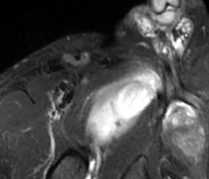
MRI of an extremity soft-tissue mass, one axial slice; position 71 of 89 along the scan axis; STIR; MR volume resampled by the dataset authors to the PET/CT grid (not the native acquisition matrix); 3.27 mm slice thickness; 209 × 179 image matrix, field of view 204 × 175 mm. Male patient. Case-level facts recorded for this patient, not image findings: histological type: undifferentiated - pleiomorphic; grade: high; site of the primary tumour: right thigh.
Outlined on this slice (expert contour drawn on MRI and transferred to this co-registered scan by the dataset authors):
- gross tumour volume including surrounding oedema: bounding box (x1, y1, x2, y2) in pixels: (87, 66, 161, 145)
- gross tumour volume (mass): (85, 71, 159, 143)